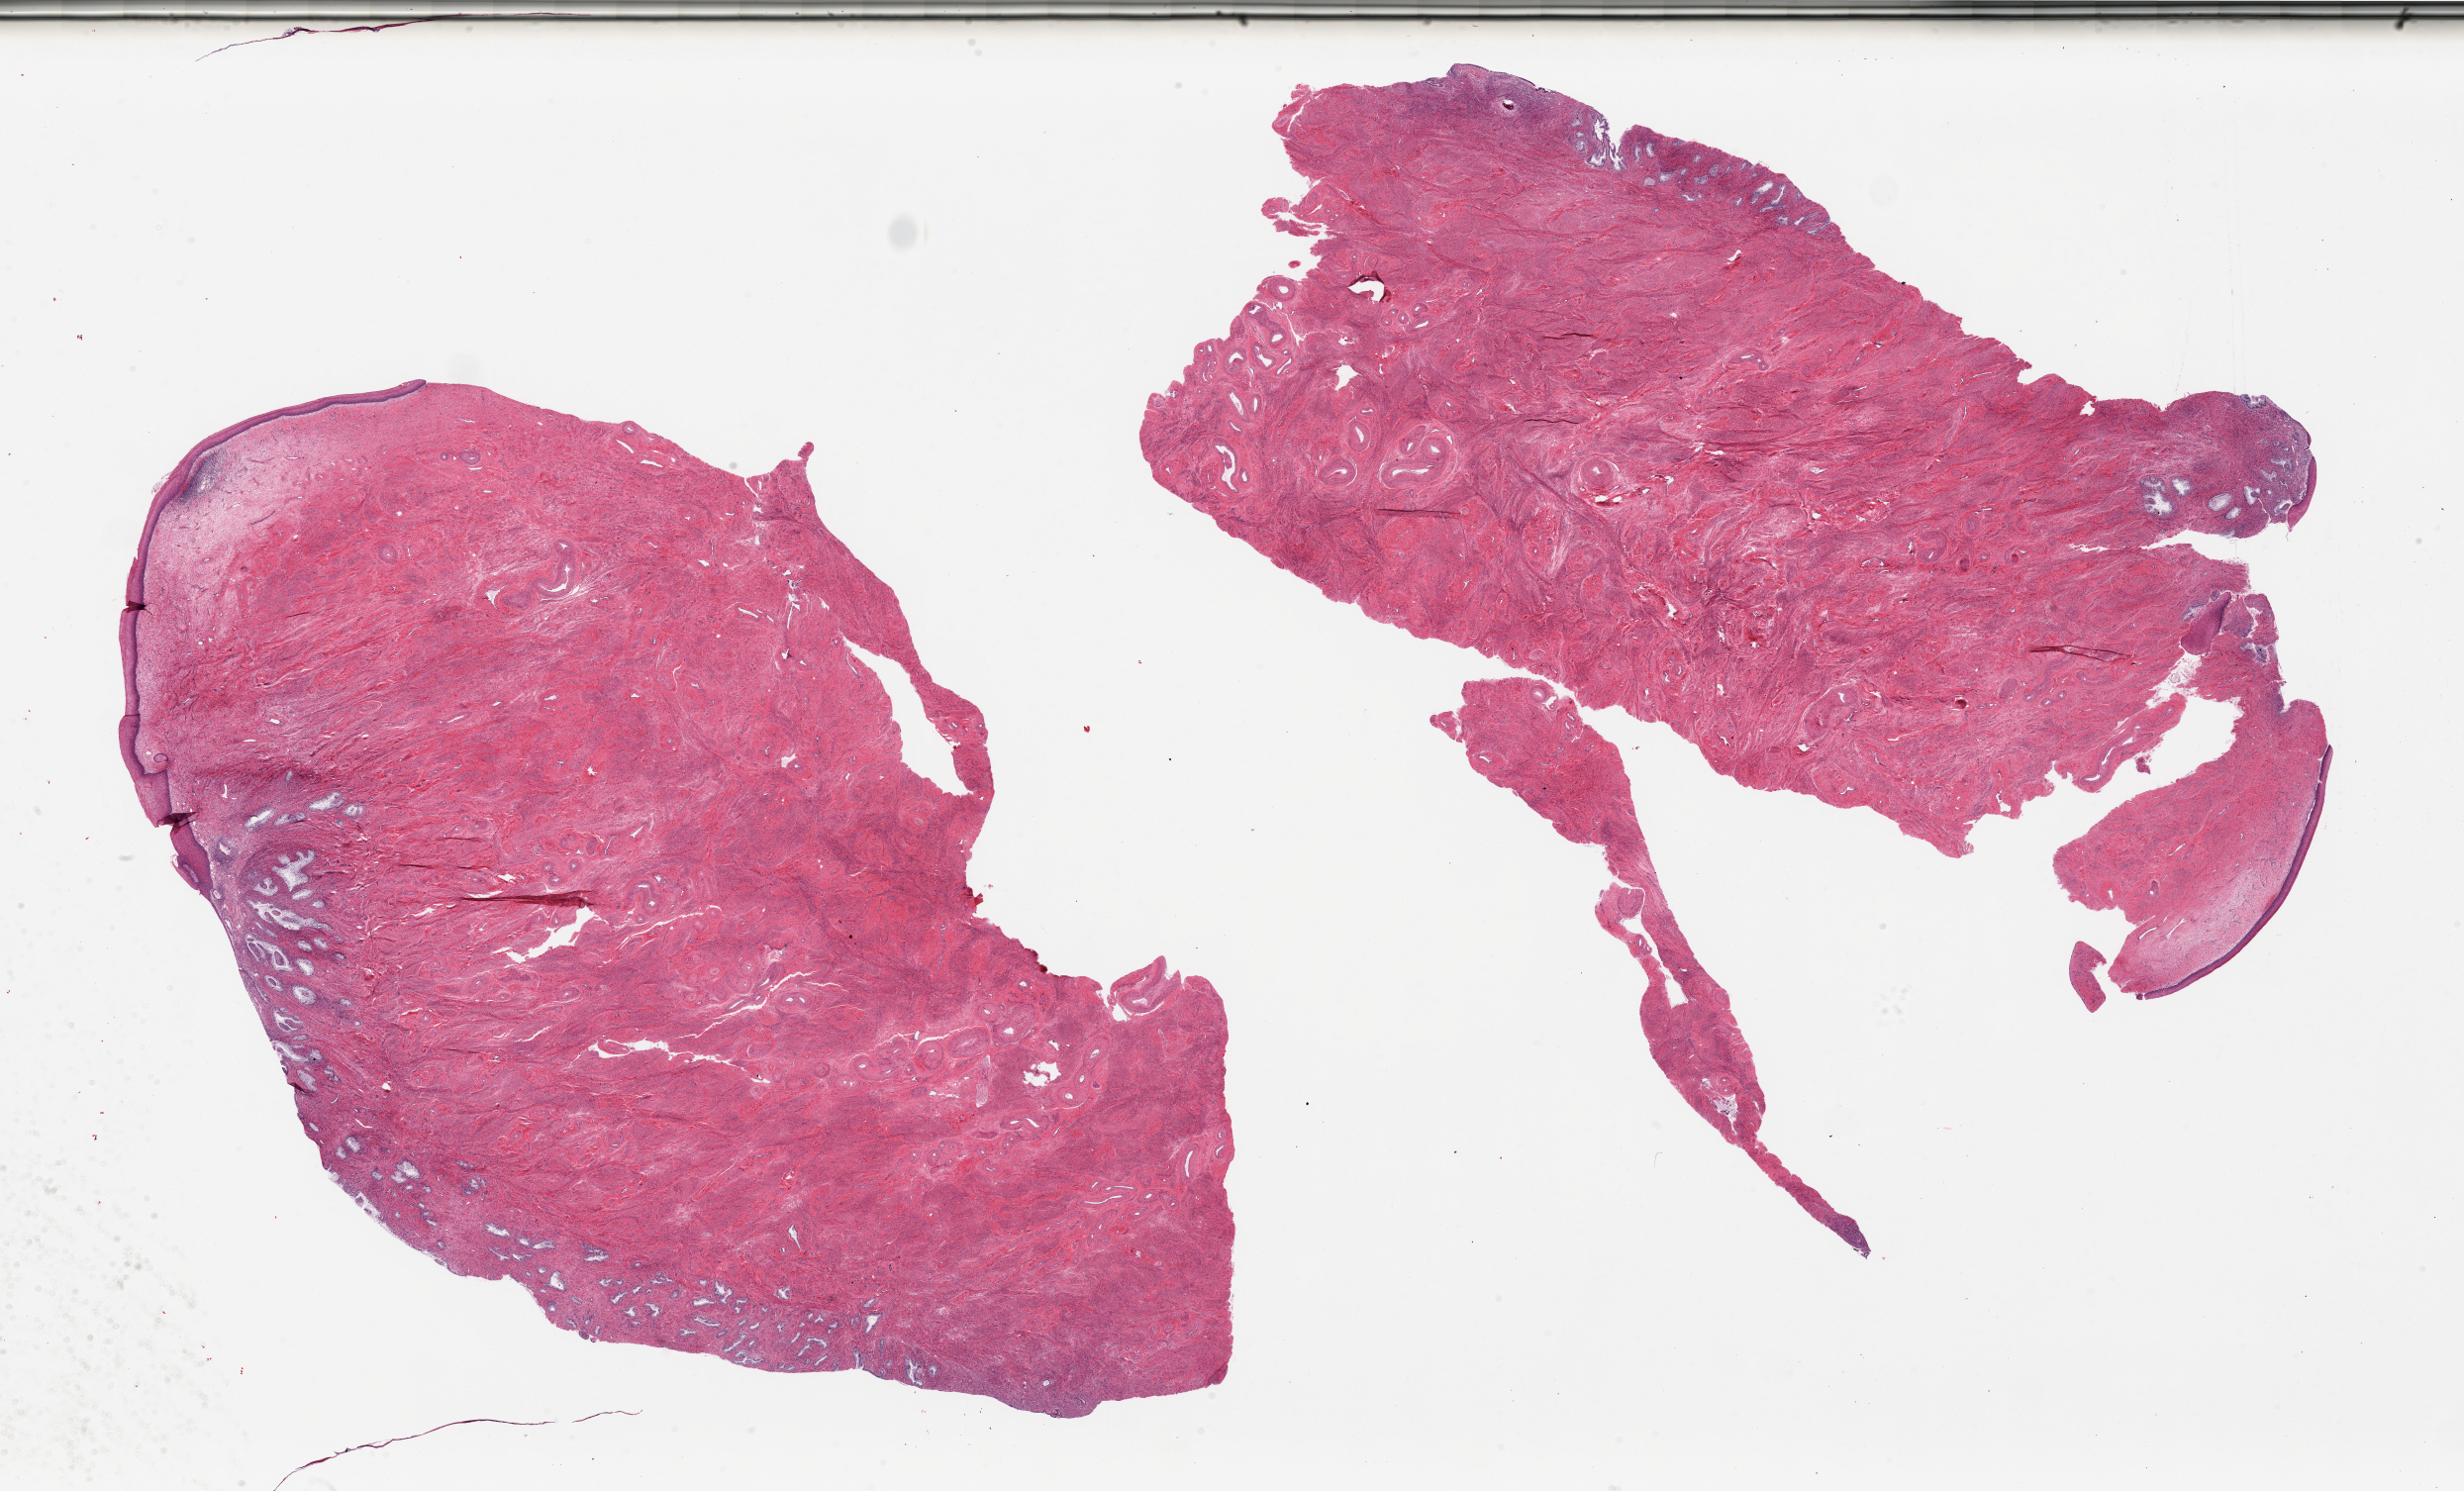
Digitized haematoxylin and eosin-stained section, brightfield — a low-resolution overview of the entire scanned area, about 39.4 x 23.8 mm (acquisition: 20x scan). PAXgene-fixed, paraffin-embedded tissue. Sampled site (target tissue): uterus. Donor tissue sample. Female donor.
Reviewer comment on this tissue sample: 2 pieces; endo and ectocervix, not uterus.